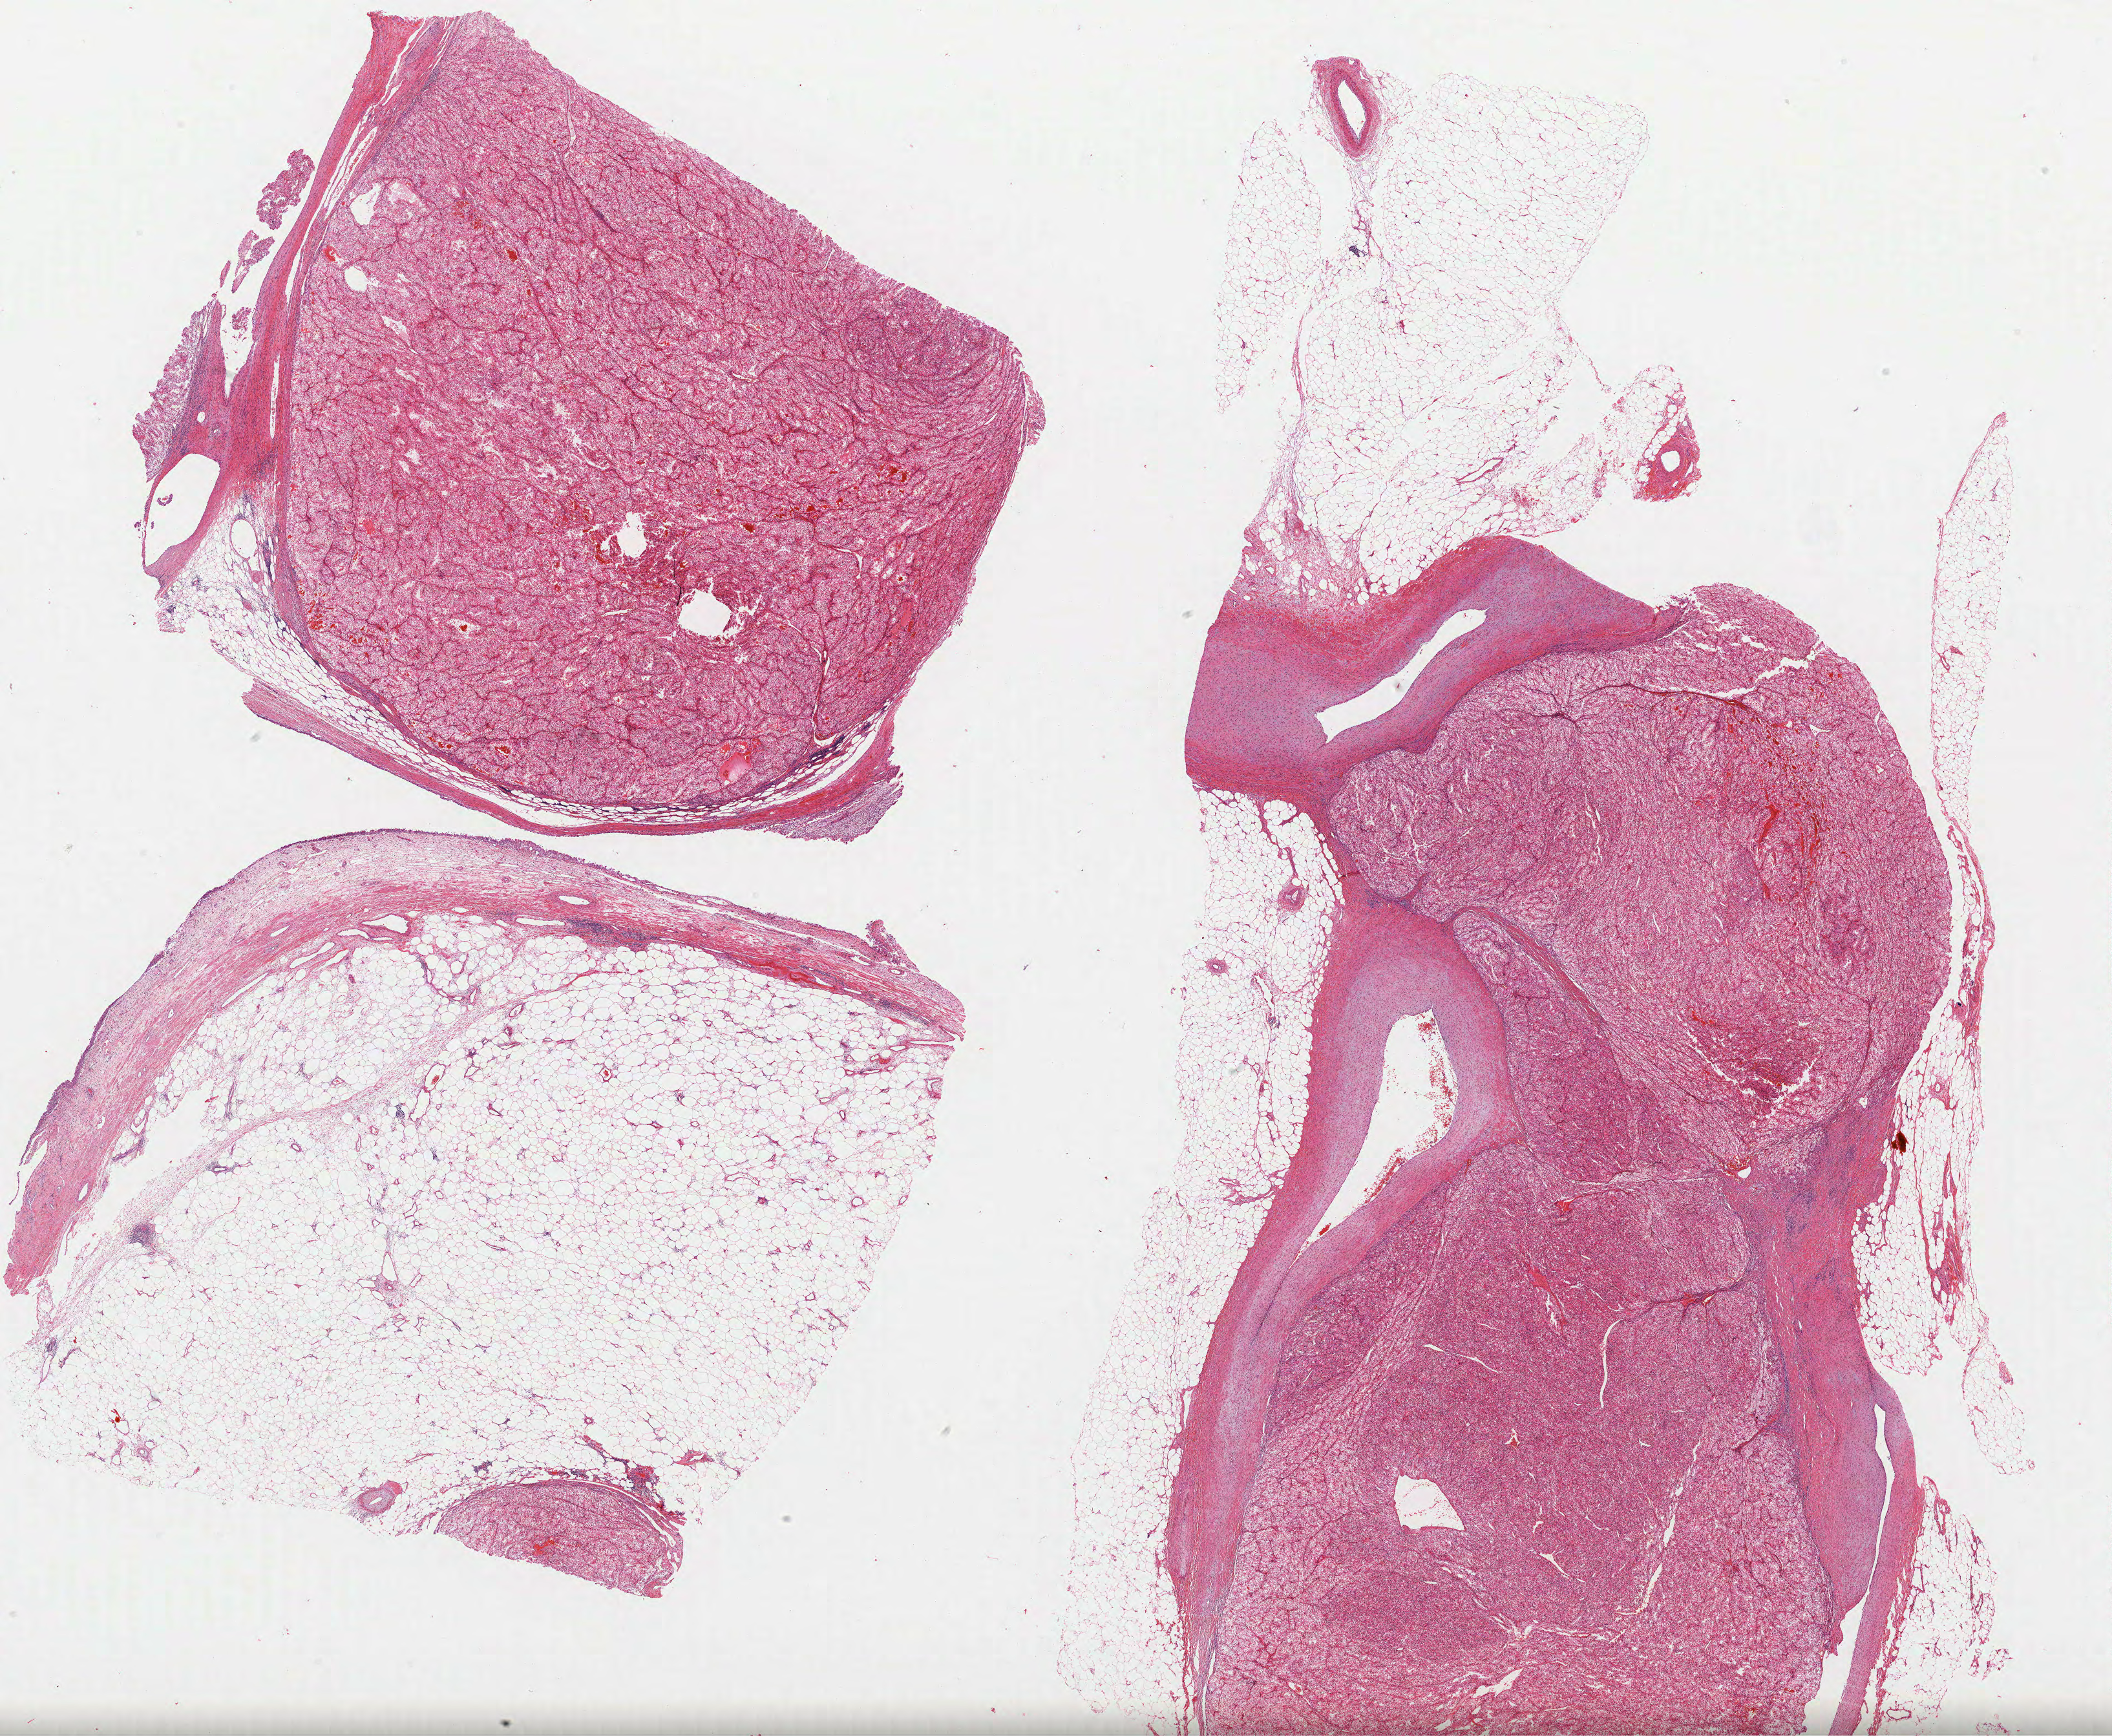
Digitized Hematoxylin and eosin (H&E) stained tissue section (whole slide) — low-resolution overview of the scanned area, about 26.3 x 21.7 mm. Formalin-fixed paraffin-embedded (FFPE) diagnostic section. Kidney, primary tumour sample. Male, age 60 years at initial diagnosis. Histologic grade: G2 (moderately differentiated).
- AJCC pathologic stage: IV (6th edition)
- laterality: right
- pathologic diagnosis: Clear cell adenocarcinoma, NOS